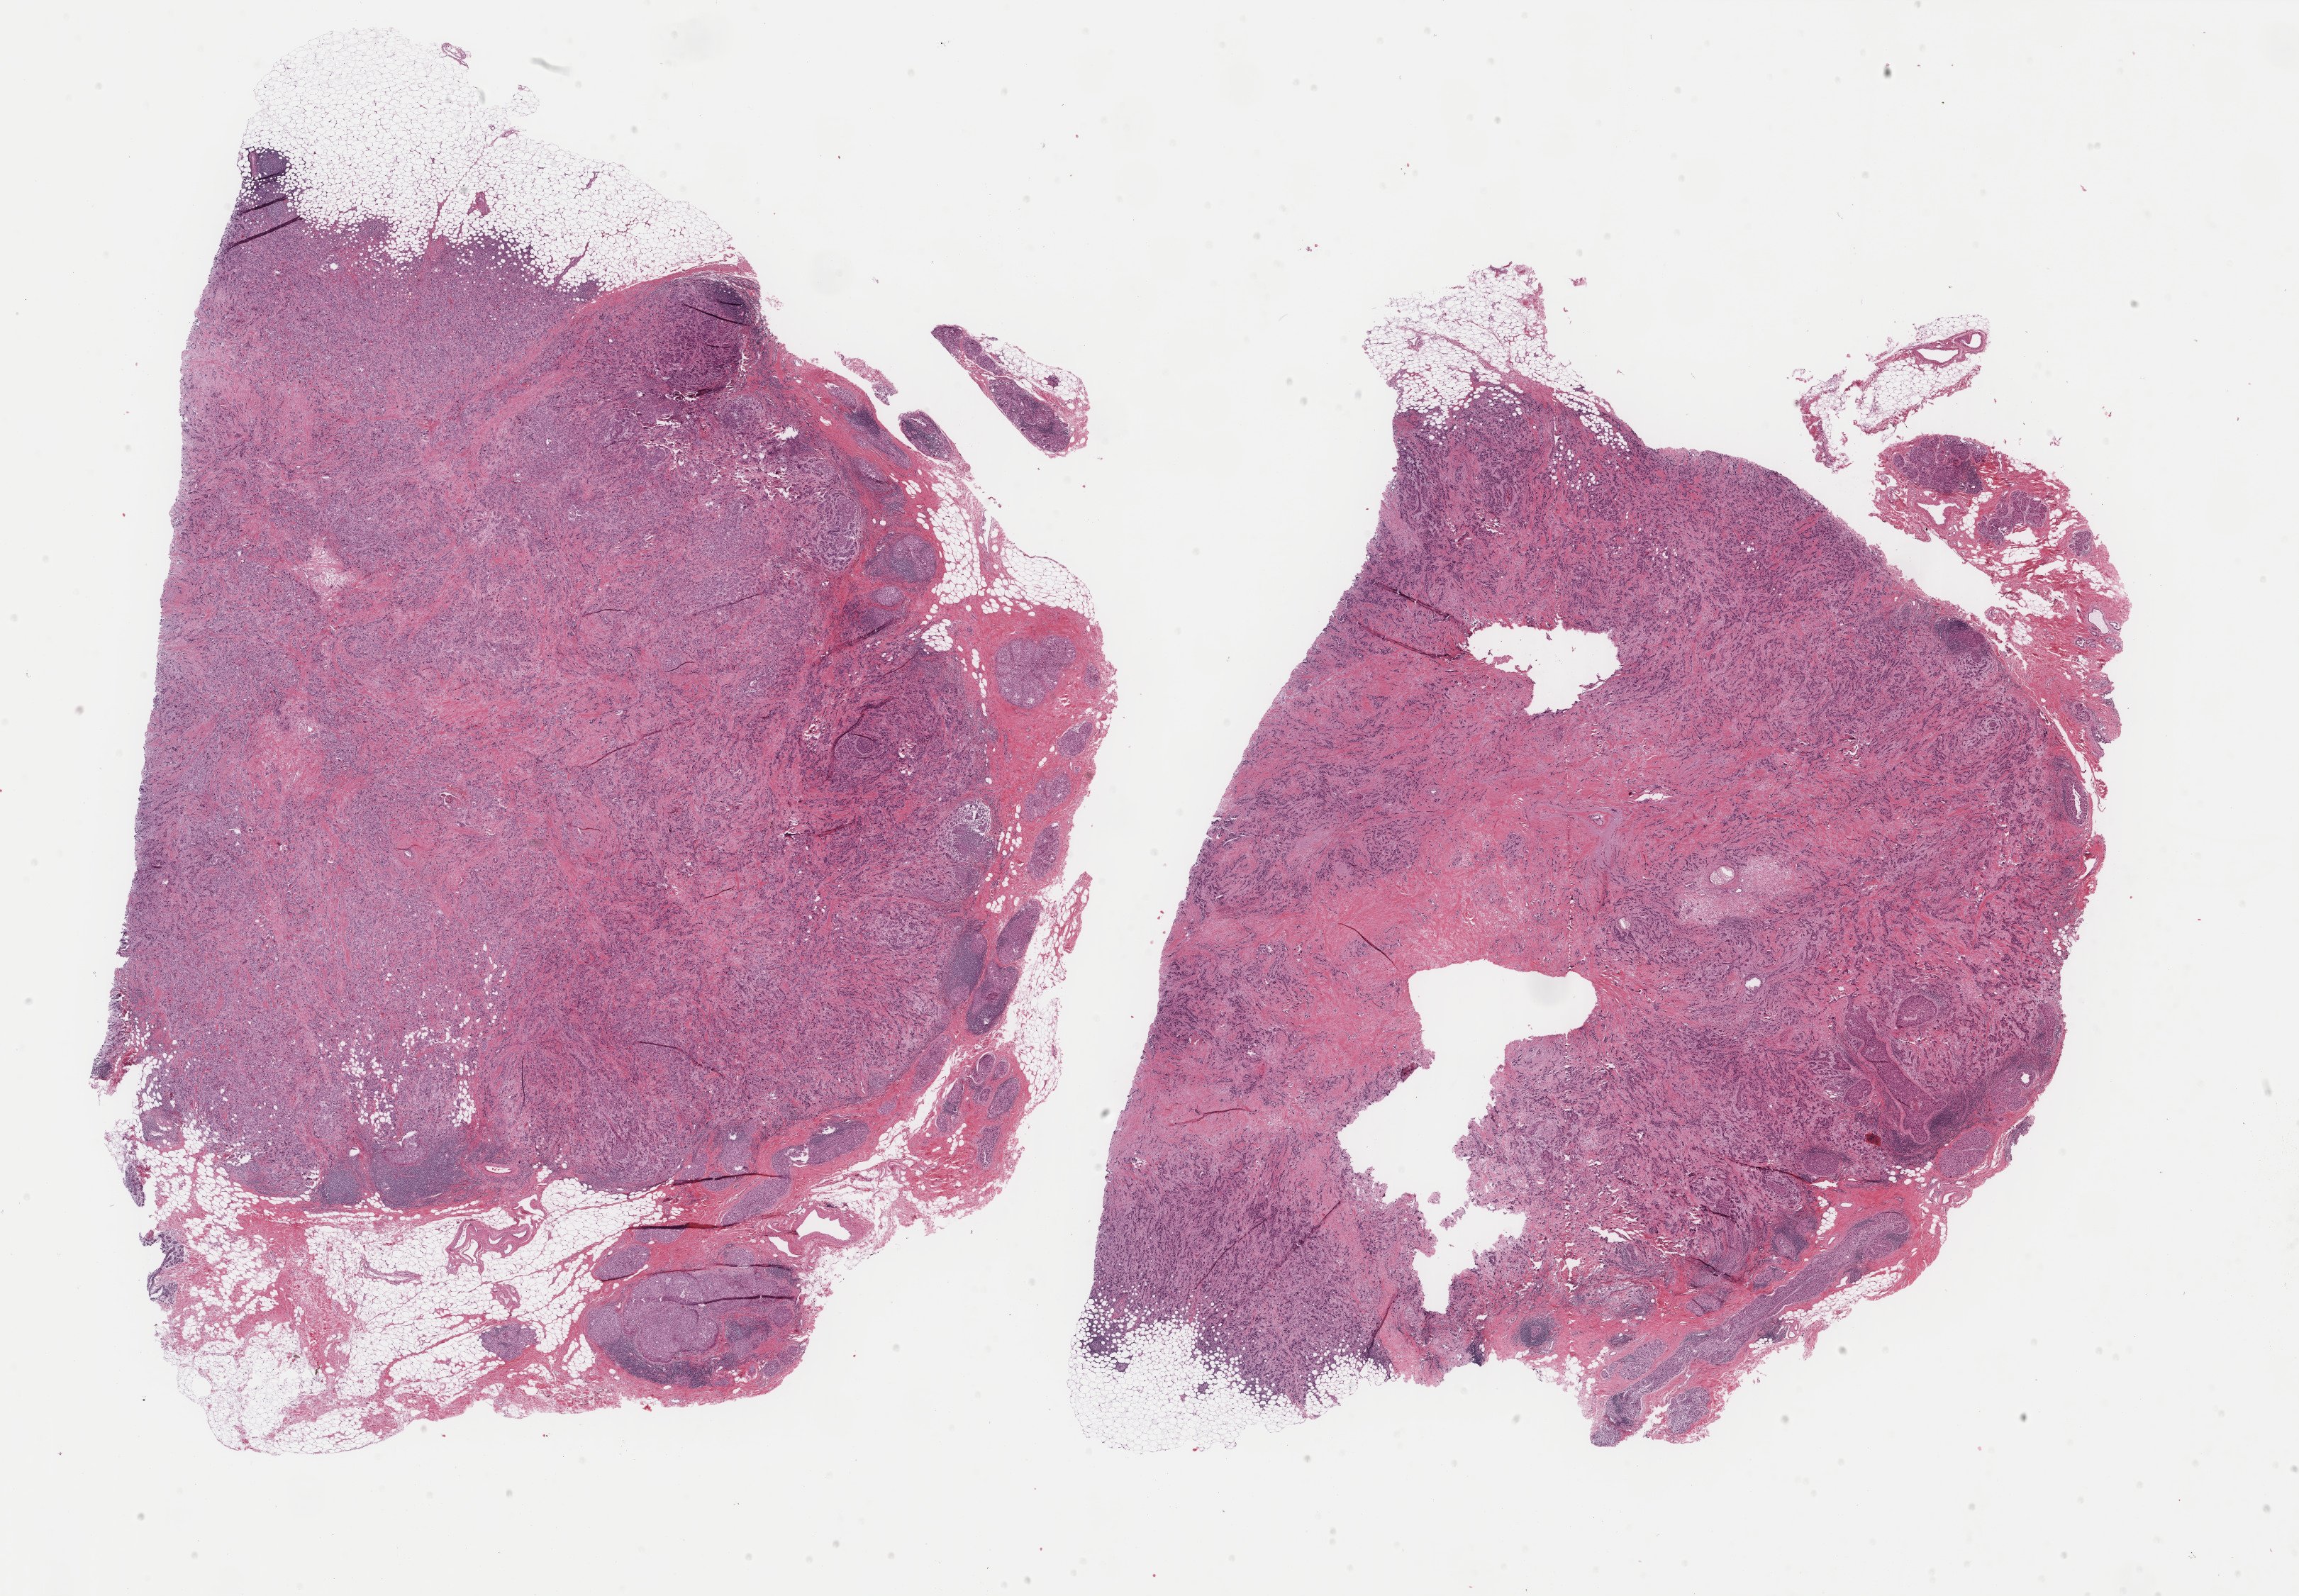
Whole-slide histology image, Hematoxylin and eosin (H&E) stained, shown as a low-resolution overview of the whole scanned area (about 25.7 x 17.9 mm); formalin-fixed paraffin-embedded (FFPE) diagnostic section; primary tumour sample from the breast. Patient: female, age at initial diagnosis 58 years.
- lymph nodes positive (case pathology): 0 of 4 examined
- AJCC pathologic stage: IIA (6th edition)
- laterality: left
- diagnosis: Infiltrating duct carcinoma, NOS